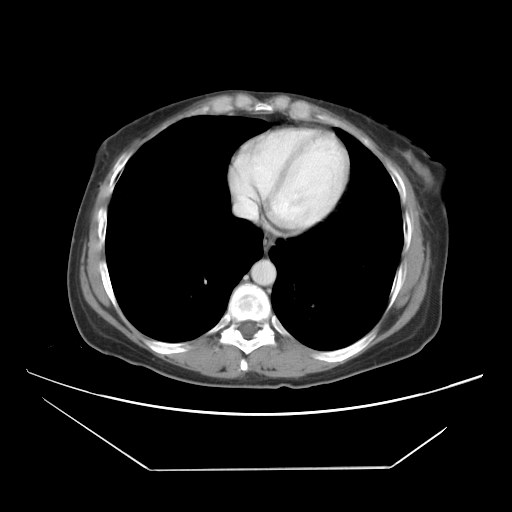
Contrast-enhanced abdominal CT, one axial slice; position 42 of 42 along the scan axis; intravenous contrast given; soft-tissue window (W 400 / L 40 HU); 5 mm slice thickness; 512 × 512 image matrix. Female patient, age 52 years. From the clinical record (not read from this slice): diagnosis: colorectal cancer liver metastases, imaged before liver resection; multiple liver metastases: yes; largest metastasis: 5.5 cm; disease in both lobes: yes.
Outlined on this slice (outlined manually by an expert reader):
- hepatic veins: bounding box [x1, y1, x2, y2] px = [237, 141, 268, 200]